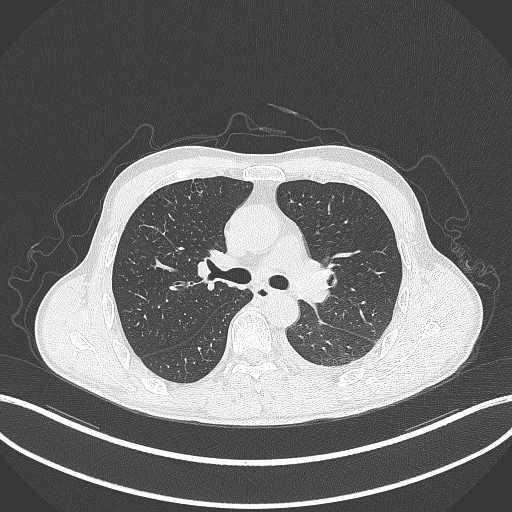
Chest CT, one axial slice; slice 208 of 295 in the series (ordered by position); 120 kVp; lung window (W 1500 / L -600 HU); 1 mm slice thickness; 512 × 512 image matrix, field of view 400 × 400 mm. Patient: male, 47 years. From the clinical record (not read from this slice): clinical TNM (as recorded): T3 N1 M1c; histopathological grade: G3.
Outlined on this slice (rectangle marked by the reading radiologist):
- lung tumour (recorded histology: small cell carcinoma): bounding box <304,283,333,305> (left, top, right, bottom; pixels)